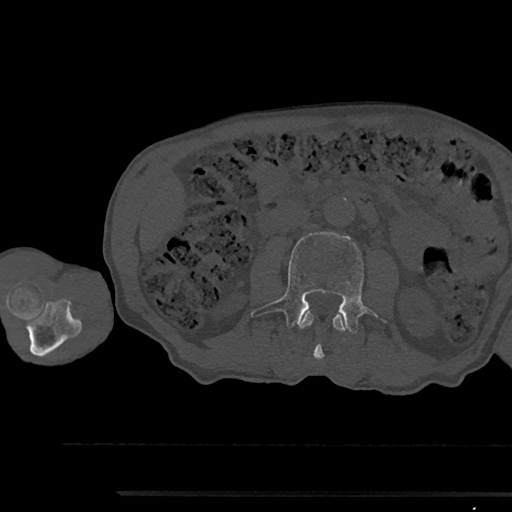
CT including the spine, one axial slice; slice 511 of 797 in the series (ordered by position); reconstruction kernel Br40s/3; bone window (W 1800 / L 400 HU); 0.5 mm slice thickness; 512 × 512 image matrix, field of view 367 × 367 mm. Patient: male, 79 years. Case-level facts recorded for this patient, not image findings: primary cancer: prostate.
Outlined on this slice (semi-automatically segmented with operator editing):
- L2 vertebra: bounding box <298,312,347,360> (left, top, right, bottom; pixels)
- L3 vertebra: <251,232,376,333>